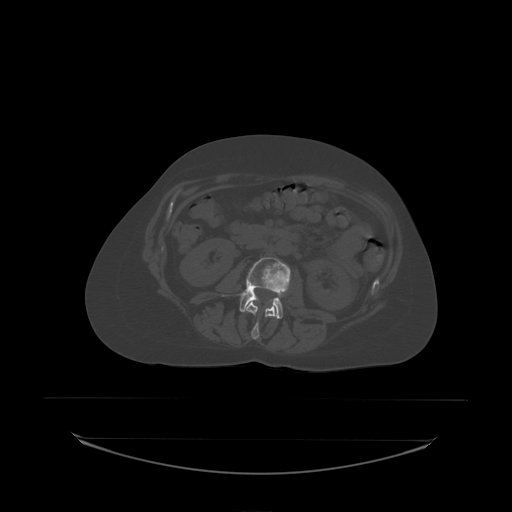
CT including the spine, one axial slice; slice 65 of 242 in the series (ordered by position); bone window (W 1800 / L 400 HU); 512 × 512 image matrix. Female patient, age 53 years. From the clinical record (not read from this slice): primary cancer: lung.
Outlined on this slice (semi-automatically segmented with operator editing):
- L2 vertebra: box from (x=245, y=302) to (x=278, y=338) px
- L3 vertebra: (x=223, y=258)–(x=291, y=319)